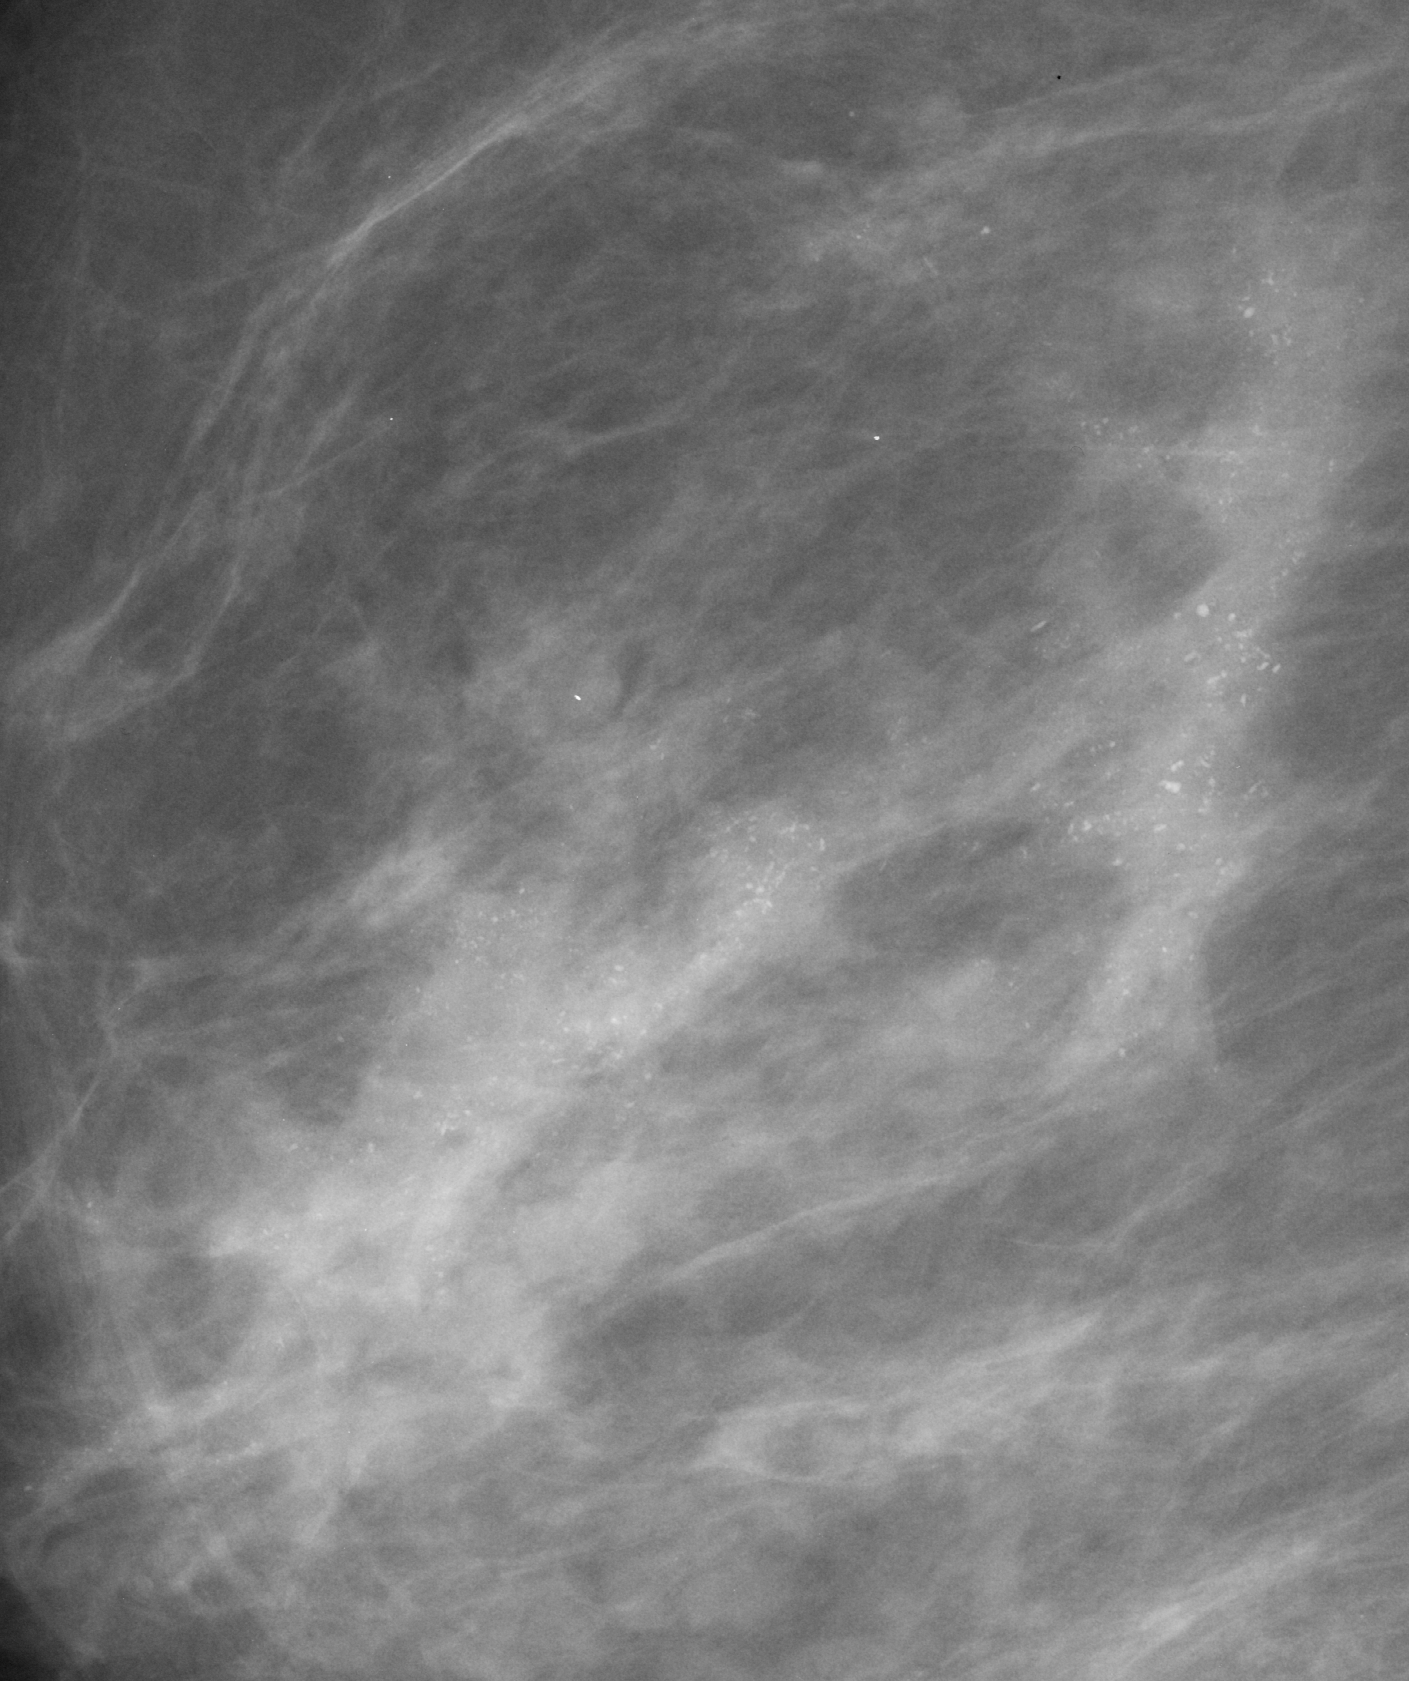
Region of interest cut from a scanned film mammogram (one marked finding); right breast; MLO view.
- Finding: calcifications, morphology pleomorphic, distribution regional; BI-RADS assessment category 5; pathology result (as recorded, not read from the image): malignant.